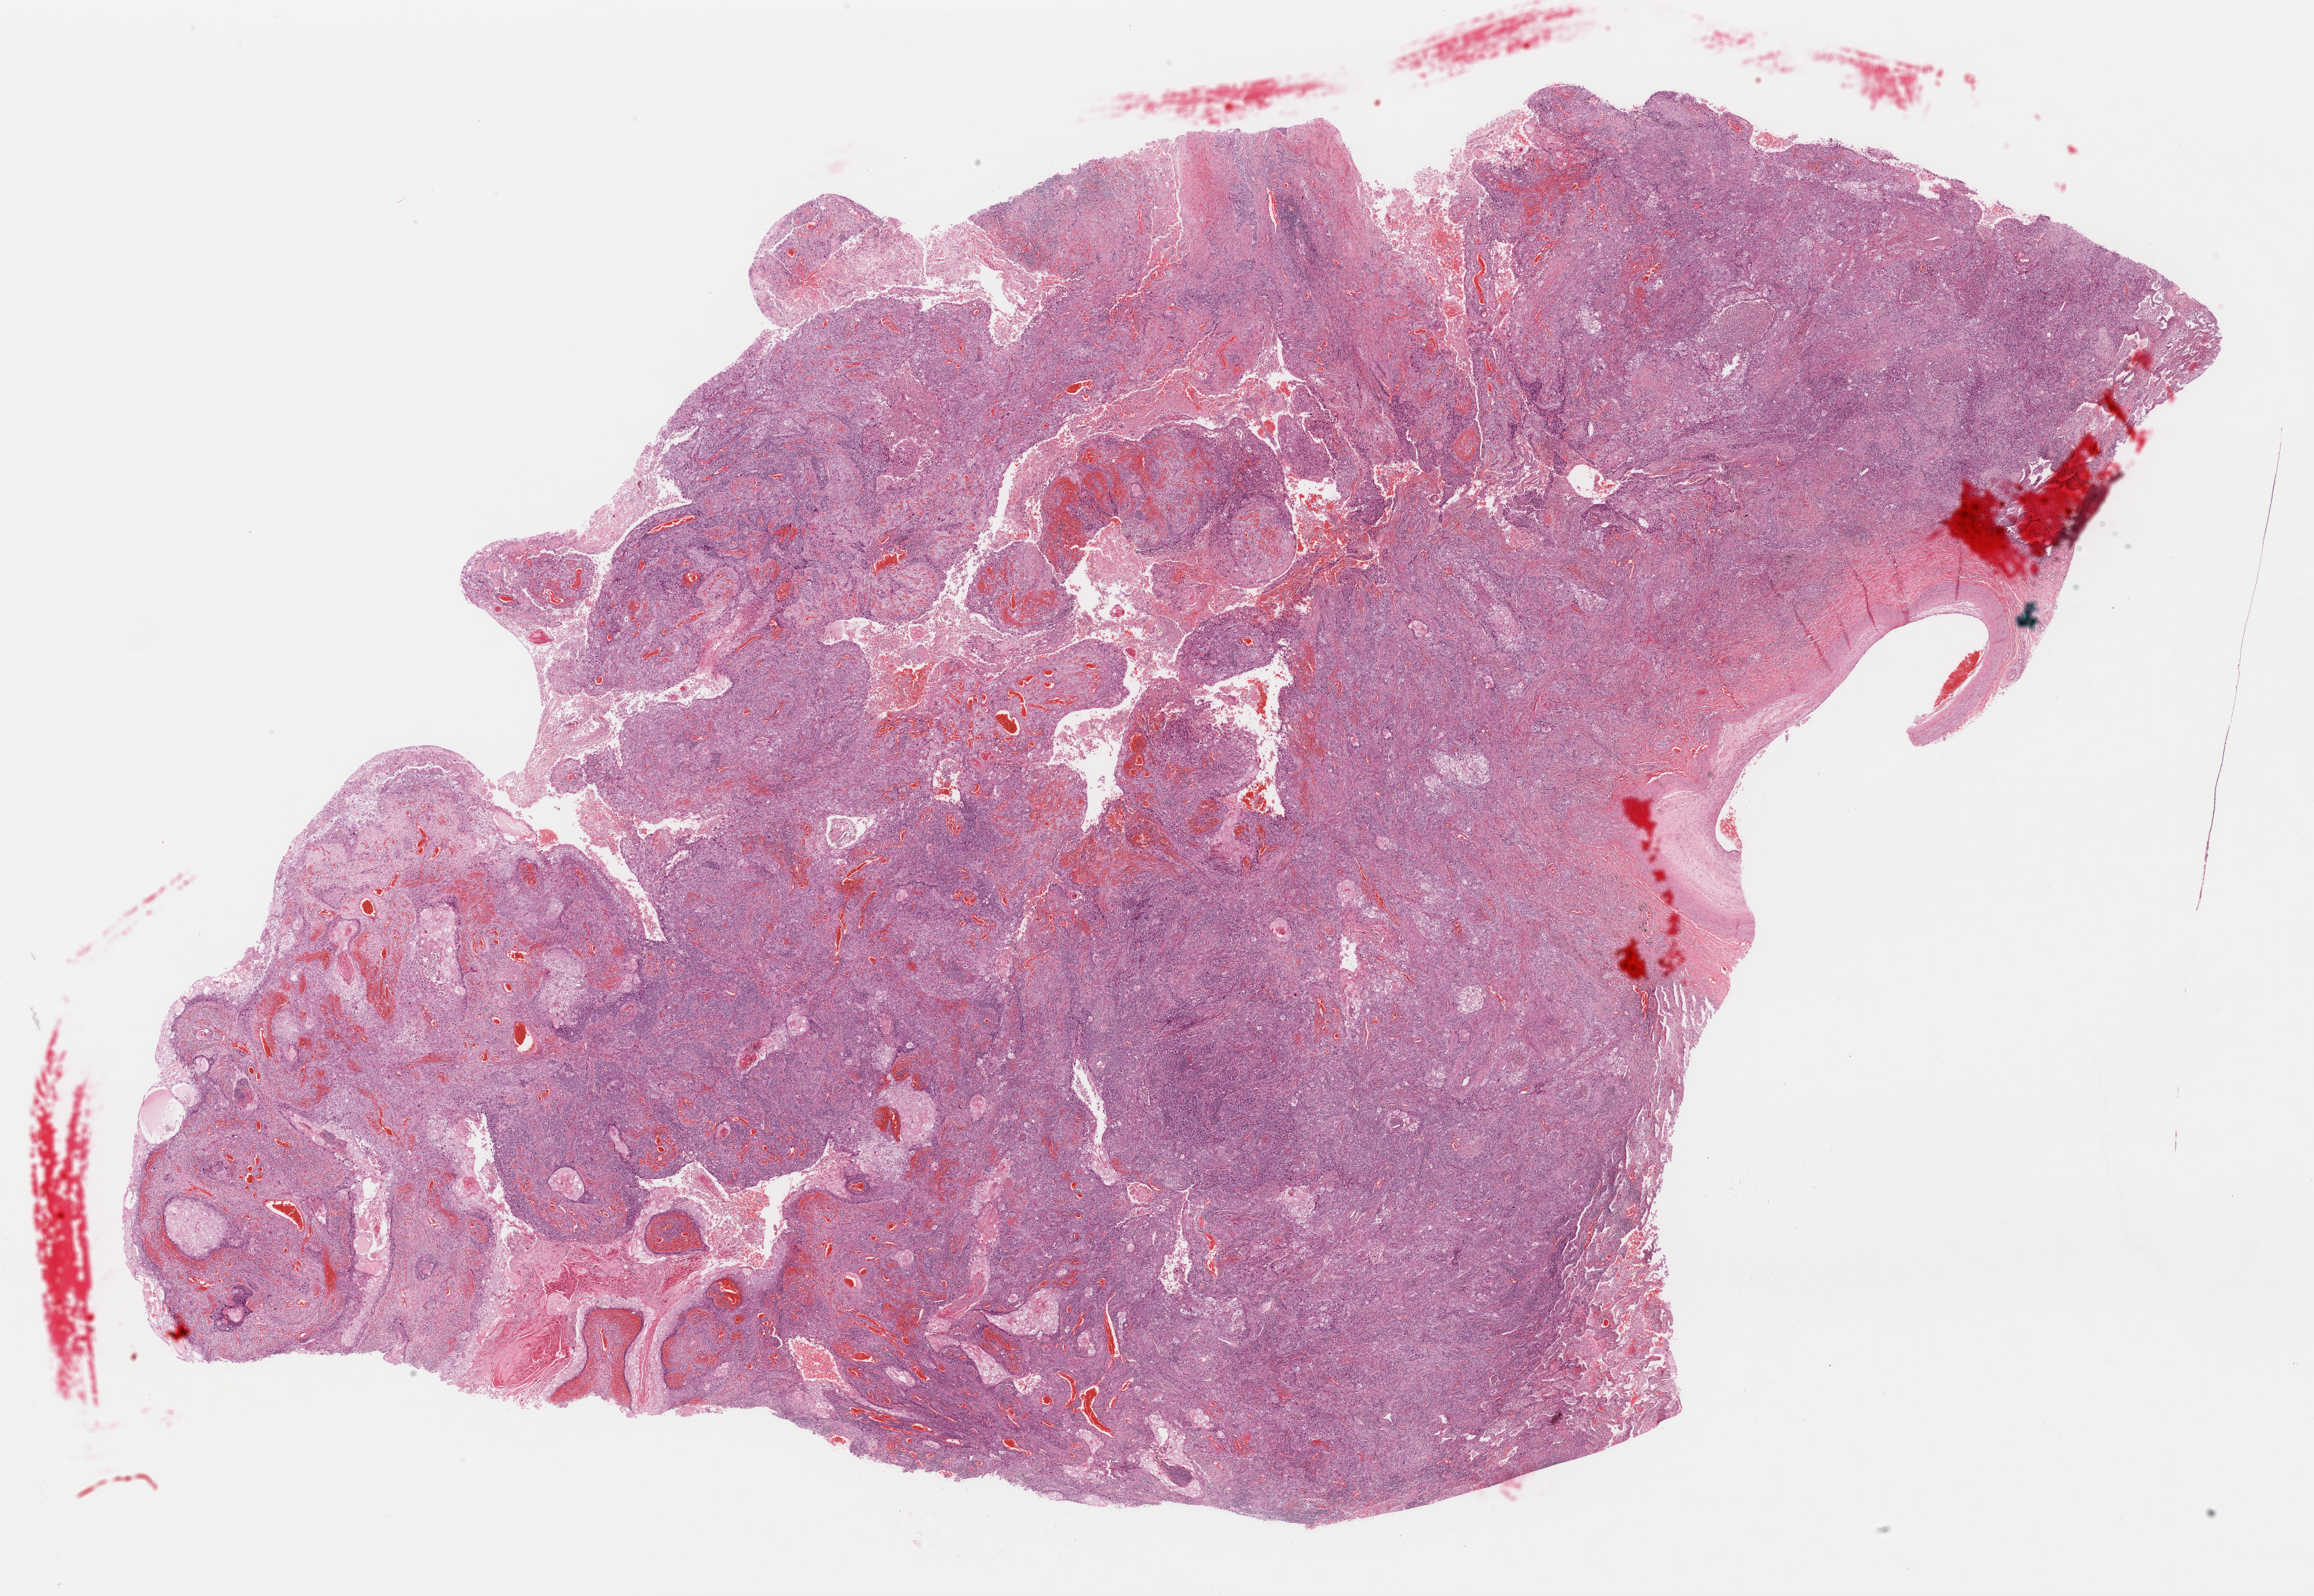
Digitized Hematoxylin and eosin (H&E) stained tissue section (whole slide), whole scanned area (about 28.4 x 19.6 mm) shown as a low-resolution overview, formalin-fixed paraffin-embedded (FFPE) diagnostic section, primary tumour sample from the lung. Male, age 74 years at initial diagnosis.
TNM: T3 N0 M0. AJCC pathologic stage: IIB (7th edition). Pathologic diagnosis: Squamous cell carcinoma, NOS (upper lobe, lung).